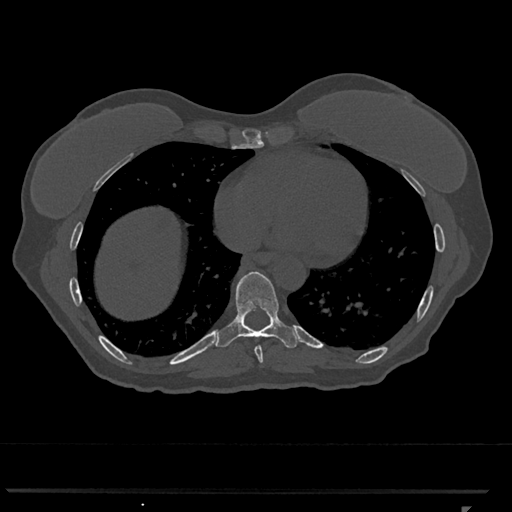
CT including the spine, one axial slice. Position 626 of 793 along the scan axis. Reconstruction kernel Br40s/3. 120 kVp. Bone window (W 1800 / L 400 HU). 0.5 mm slice thickness. 512 × 512 image matrix, field of view 380 × 380 mm. Patient: female, 62 years. Case-level facts recorded for this patient, not image findings: primary cancer: renal.
Structures marked on this image (semi-automatic segmentation, software-assisted and operator-edited):
- T8 vertebra: bounding box (x1, y1, x2, y2) in pixels: (254, 346, 263, 363)
- T9 vertebra: (215, 271, 299, 348)